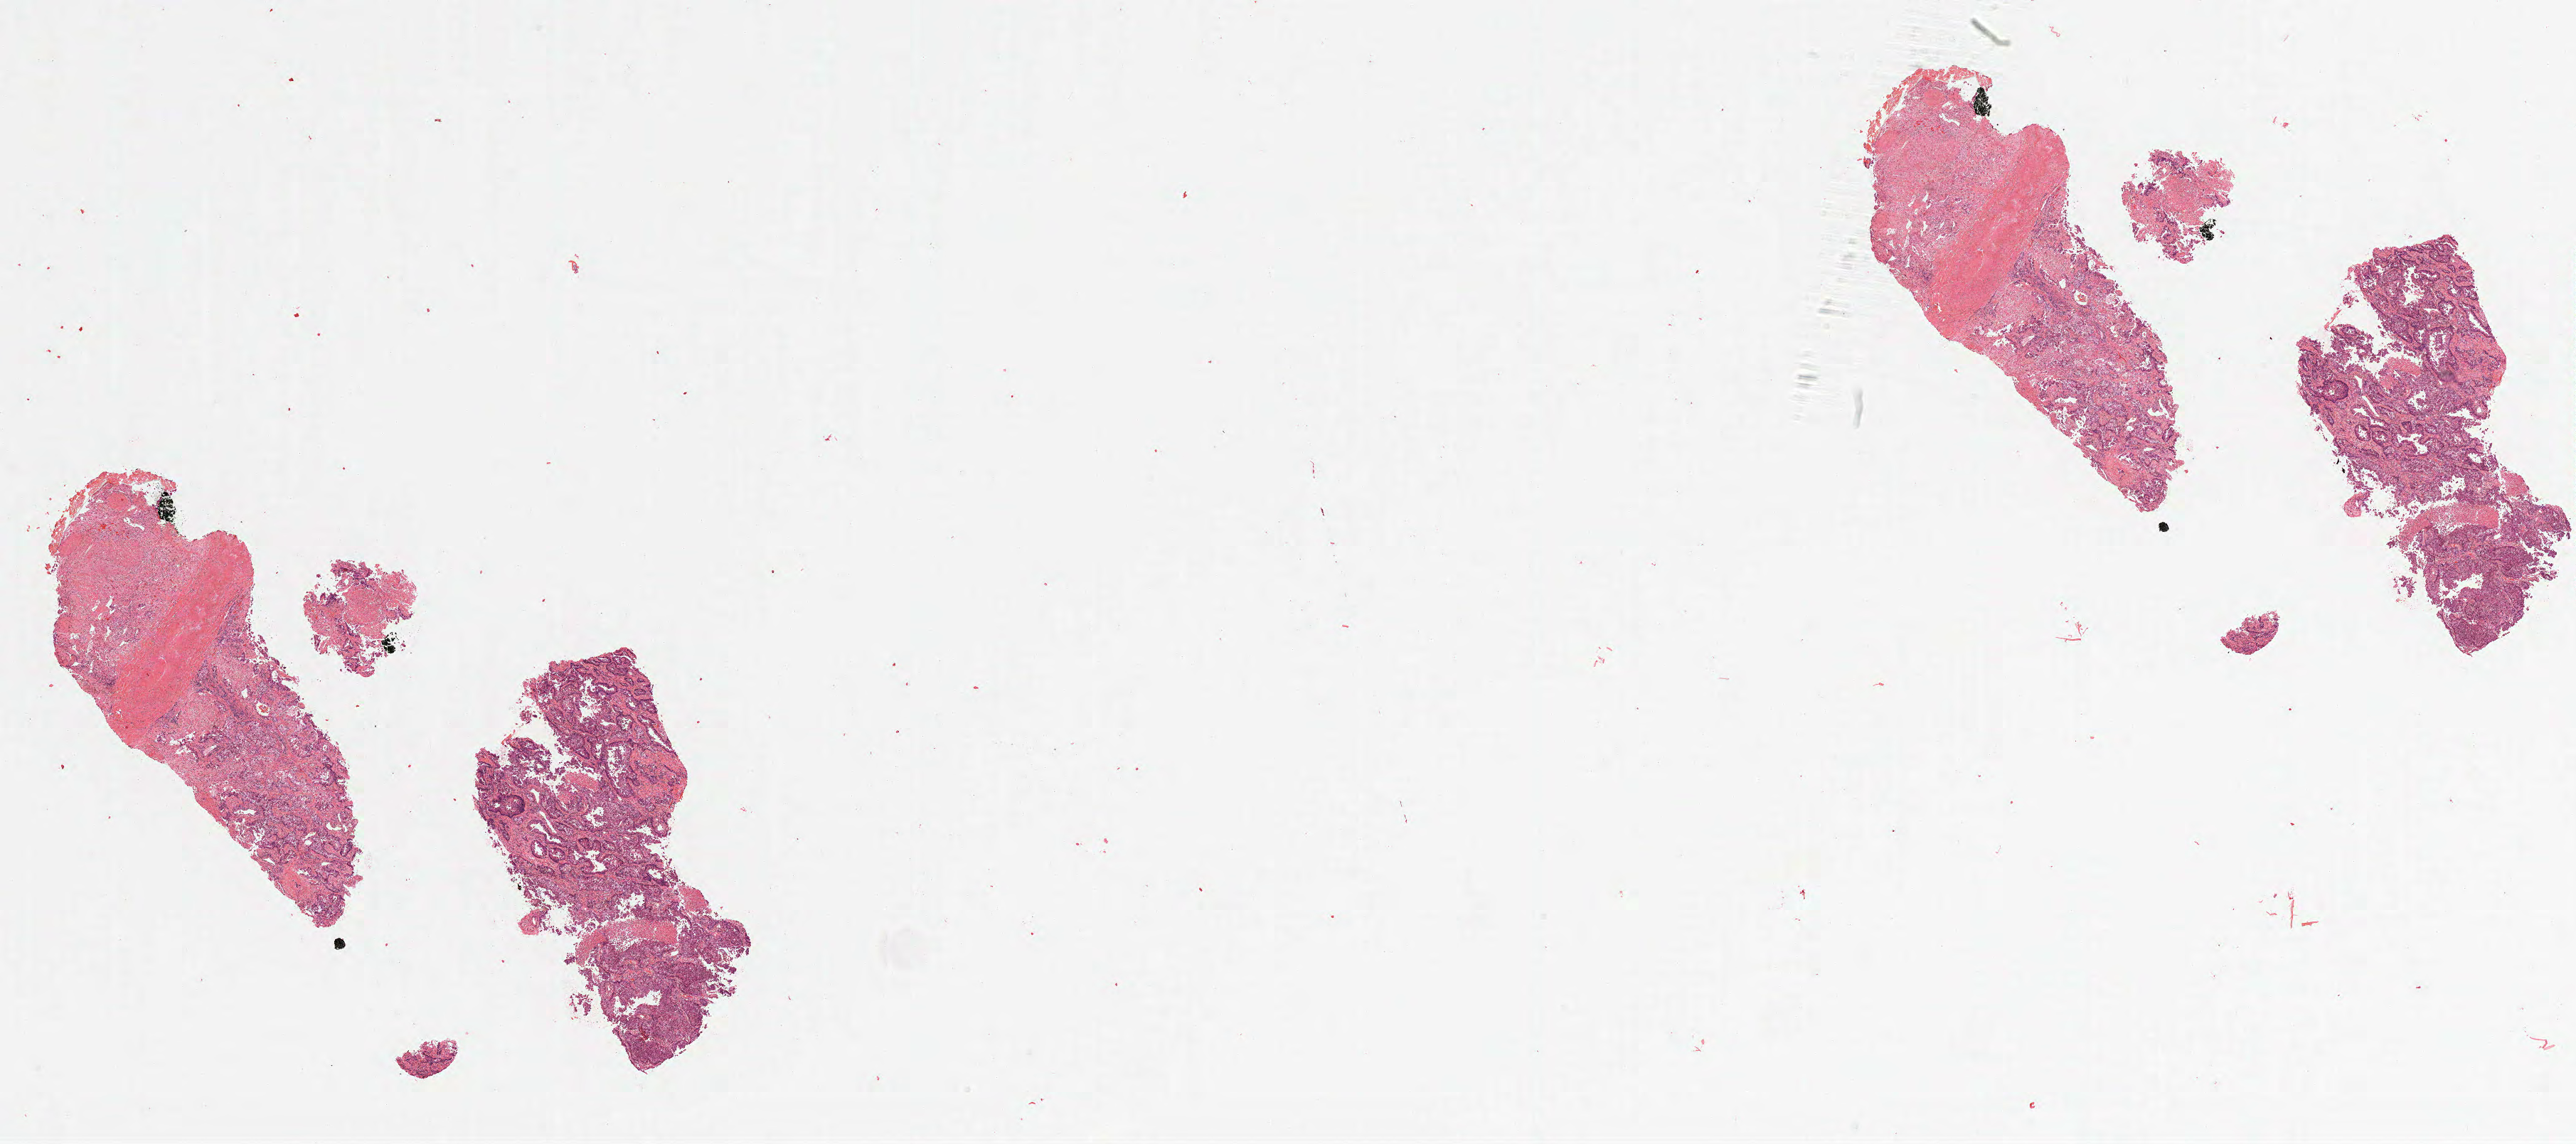
Hematoxylin and eosin (H&E) stained whole-slide image — a low-resolution overview of the entire scanned area, about 29.0 x 12.9 mm (slide scanned at 20x), formalin-fixed paraffin-embedded (FFPE) diagnostic section, primary tumour sample from the lung. Patient sex: female.
AJCC pathologic stage: IB. Diagnosis: Adenocarcinoma, NOS.